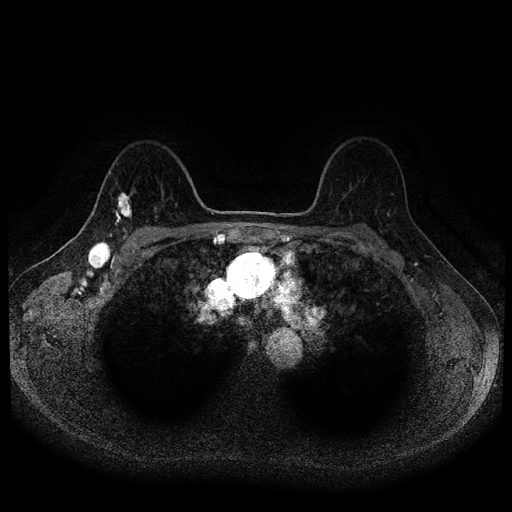
Breast MRI (dynamic contrast-enhanced, multi-phase), one axial slice; position 73 of 116 along the scan axis; dynamic contrast-enhanced series, time point 2 of 5 at this slice position (early post-contrast); 1.5 T; TE 2.6 ms, TR 5.4 ms; 512 × 512 image matrix, field of view 340 × 340 mm. Patient: female, 49 years.
Outlined on this slice (semi-automatically segmented with operator editing):
- breast lesion (labelled 'tumour' in the annotation; benign lesions carry a separate 'benign' label): bounding box (x1, y1, x2, y2) in pixels: (112, 188, 136, 230)